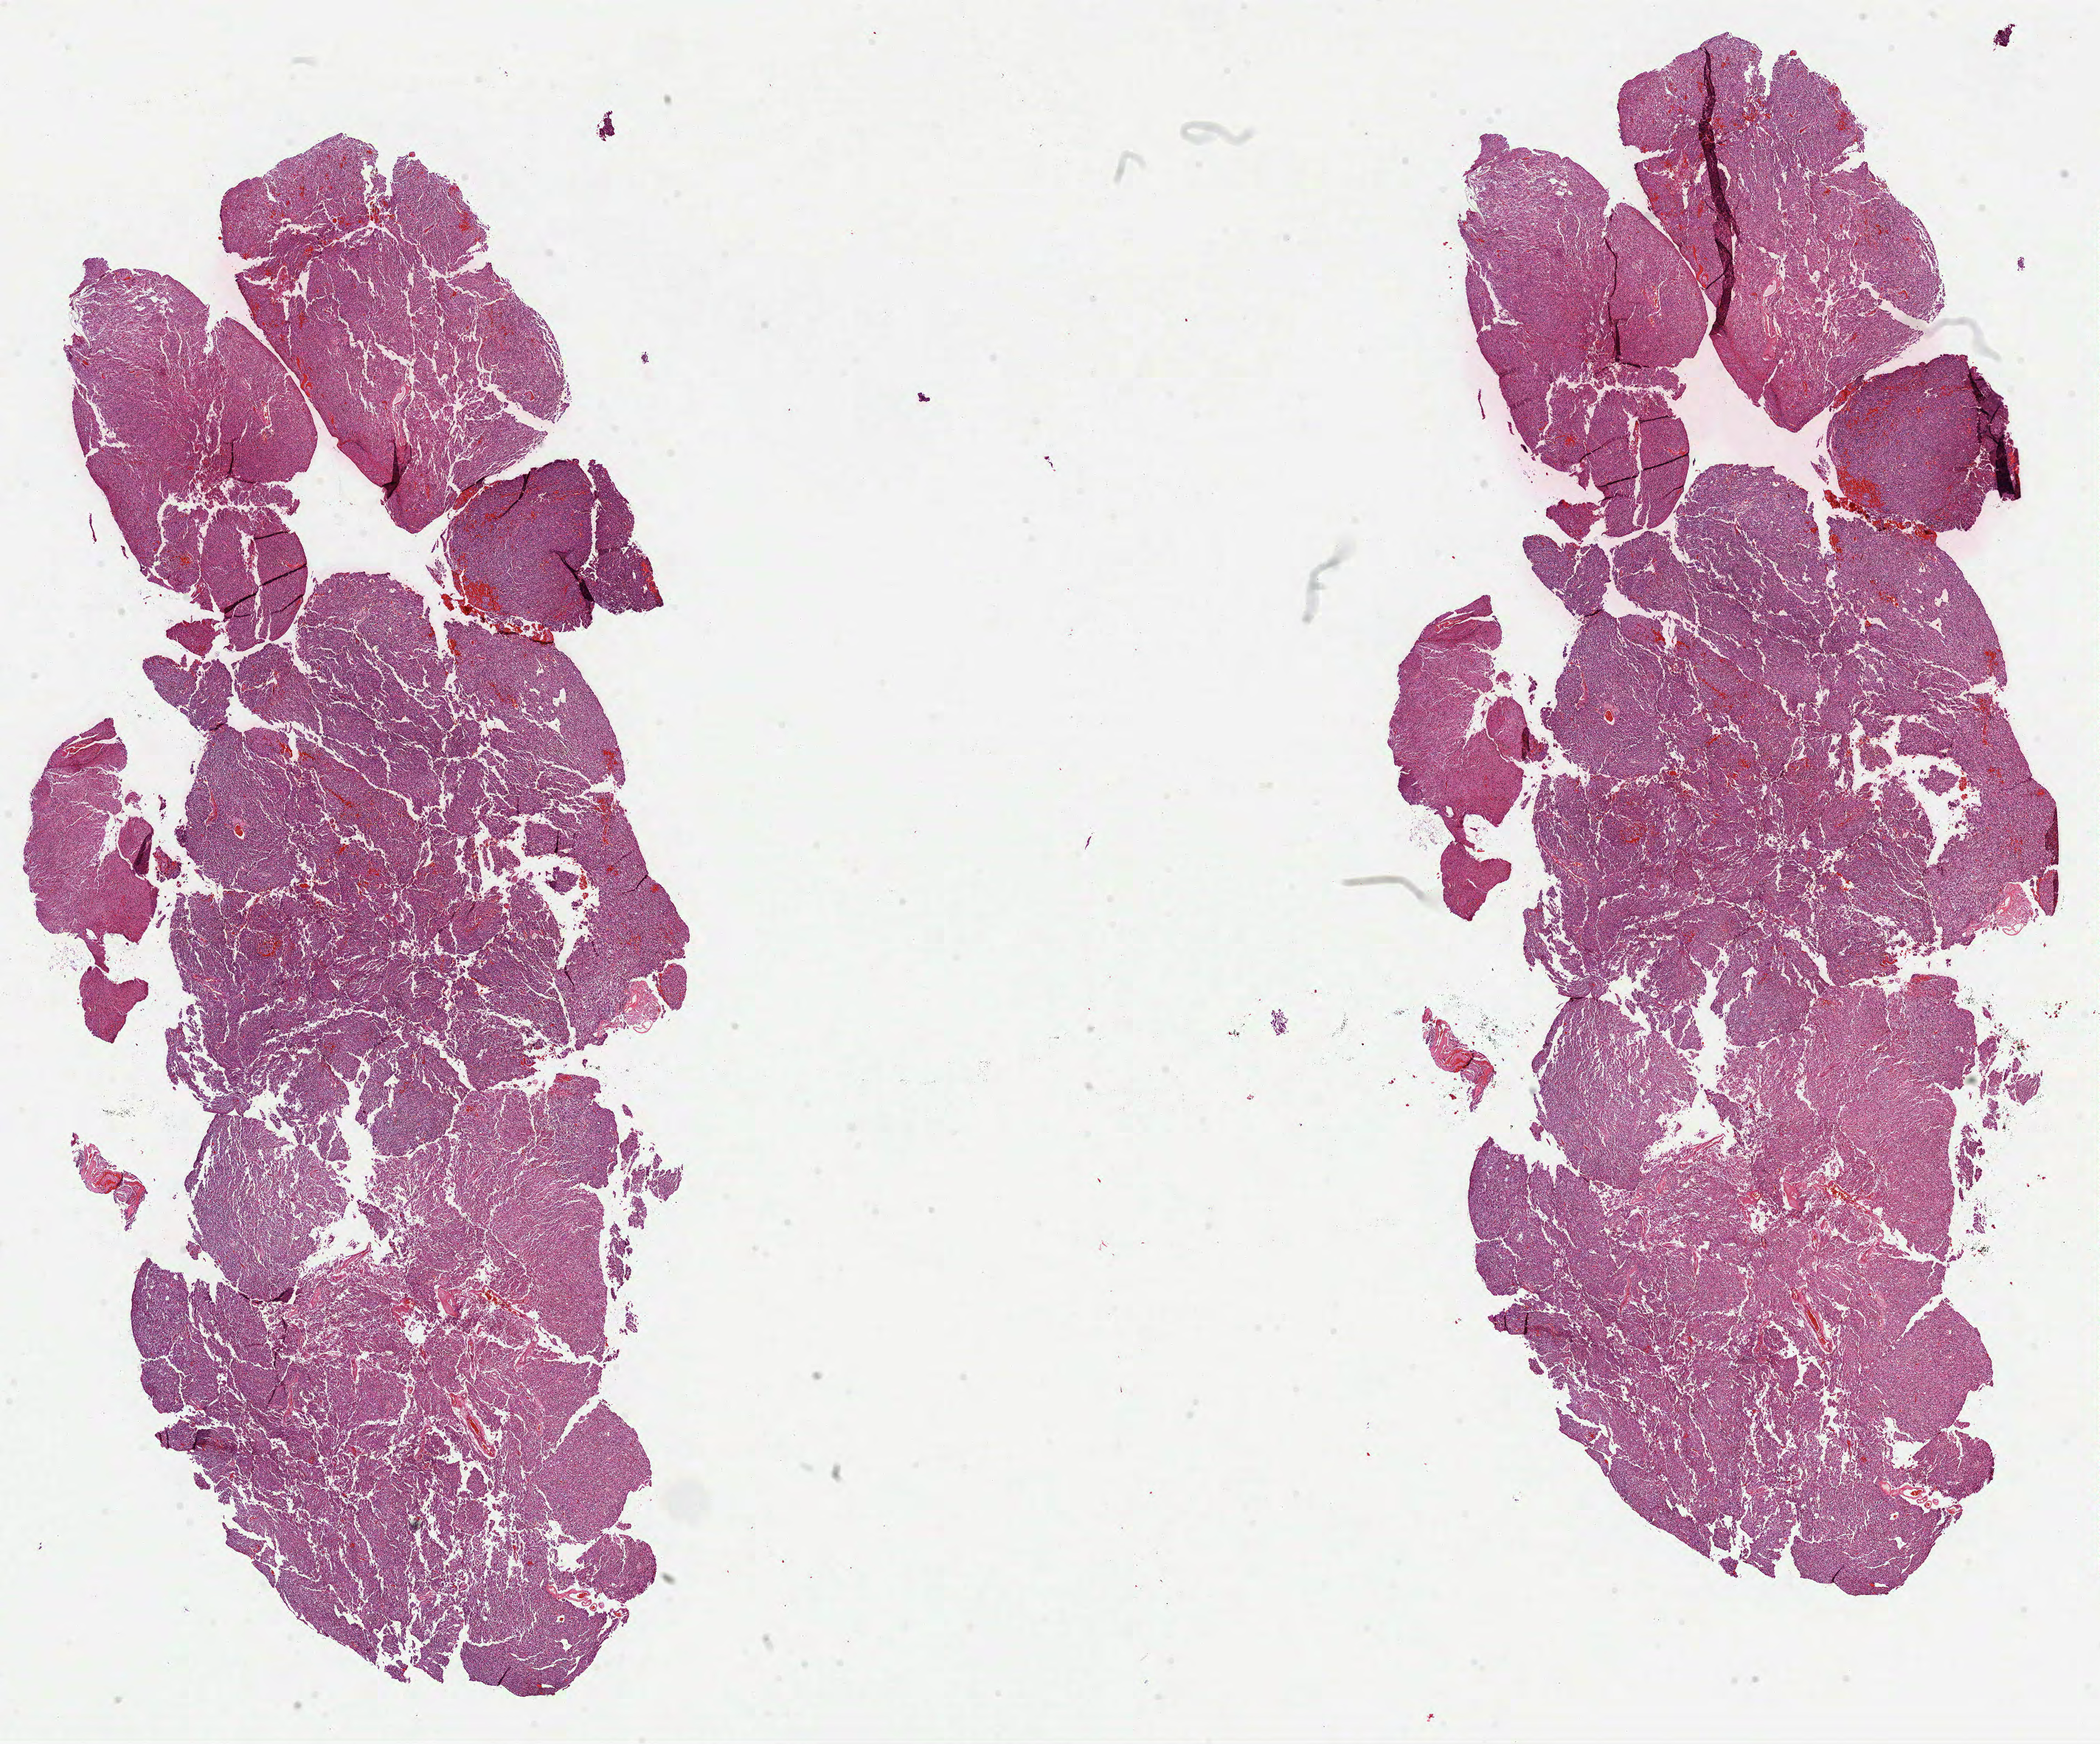
Whole-slide histology image, Hematoxylin and eosin (H&E) stained, whole scanned area (about 23.0 x 19.1 mm, from a 40x scan) shown as a low-resolution overview; formalin-fixed paraffin-embedded (FFPE) diagnostic section; sample: primary tumour, brain. Patient: male, age at initial diagnosis 40 years. Histologic grade: G3 (poorly differentiated).
Laterality: left. Histologic diagnosis: Astrocytoma, anaplastic.